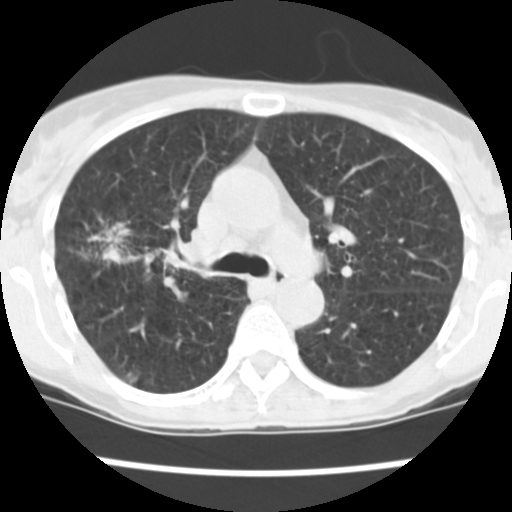
Chest CT (low-dose screening protocol), one axial image; baseline screening round; lung window (W 1500 / L -600 HU); 2.5 mm slice thickness; standard (soft-tissue) reconstruction kernel (STANDARD); slice 160 of 252 in the series; 512 × 512 image matrix. Female participant, aged 60 years at enrolment. Current smoker at enrolment.
• Expert-annotated lung lesion, bounding box <81,215,188,282> (left, top, right, bottom; pixels).
• The screening reader recorded 3 non-calcified nodules or masses ≥4 mm on this exam (right upper lobe, right upper lobe, right lower lobe); which of them this box marks is not recorded.
• Official screen result: positive, change unspecified: nodule(s) >= 4 mm or enlarging nodule(s), mass(es), or other non-specific abnormalities suspicious for lung cancer.
• Participant outcome: lung cancer diagnosed 19 days after this screen — non-small cell carcinoma, right upper lobe, stage IV (AJCC 6th edition), 26 mm at pathology.